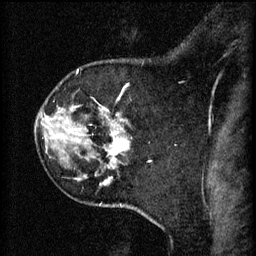
Breast MRI (dynamic contrast-enhanced), one sagittal slice. Slice 49 of 60 in the series (ordered by position). 3 images stored at this slice position (order not interpretable as contrast timing). 1.5 T. TE 4.2 ms, TR 11 ms. 2 mm slice thickness. 256 × 256 image matrix, field of view 180 × 180 mm. Female patient, age 45 years.
Annotated regions visible in this slice (semi-automatic segmentation, software-assisted and operator-edited):
- analysis volume of interest (the breast-tissue region the enhancement analysis was run in; not a lesion): bounding box [x1, y1, x2, y2] px = [106, 128, 127, 171]
- tumour enhancement mask (voxels above the 70 % enhancement threshold inside the analysis volume of interest): [110, 132, 127, 155]